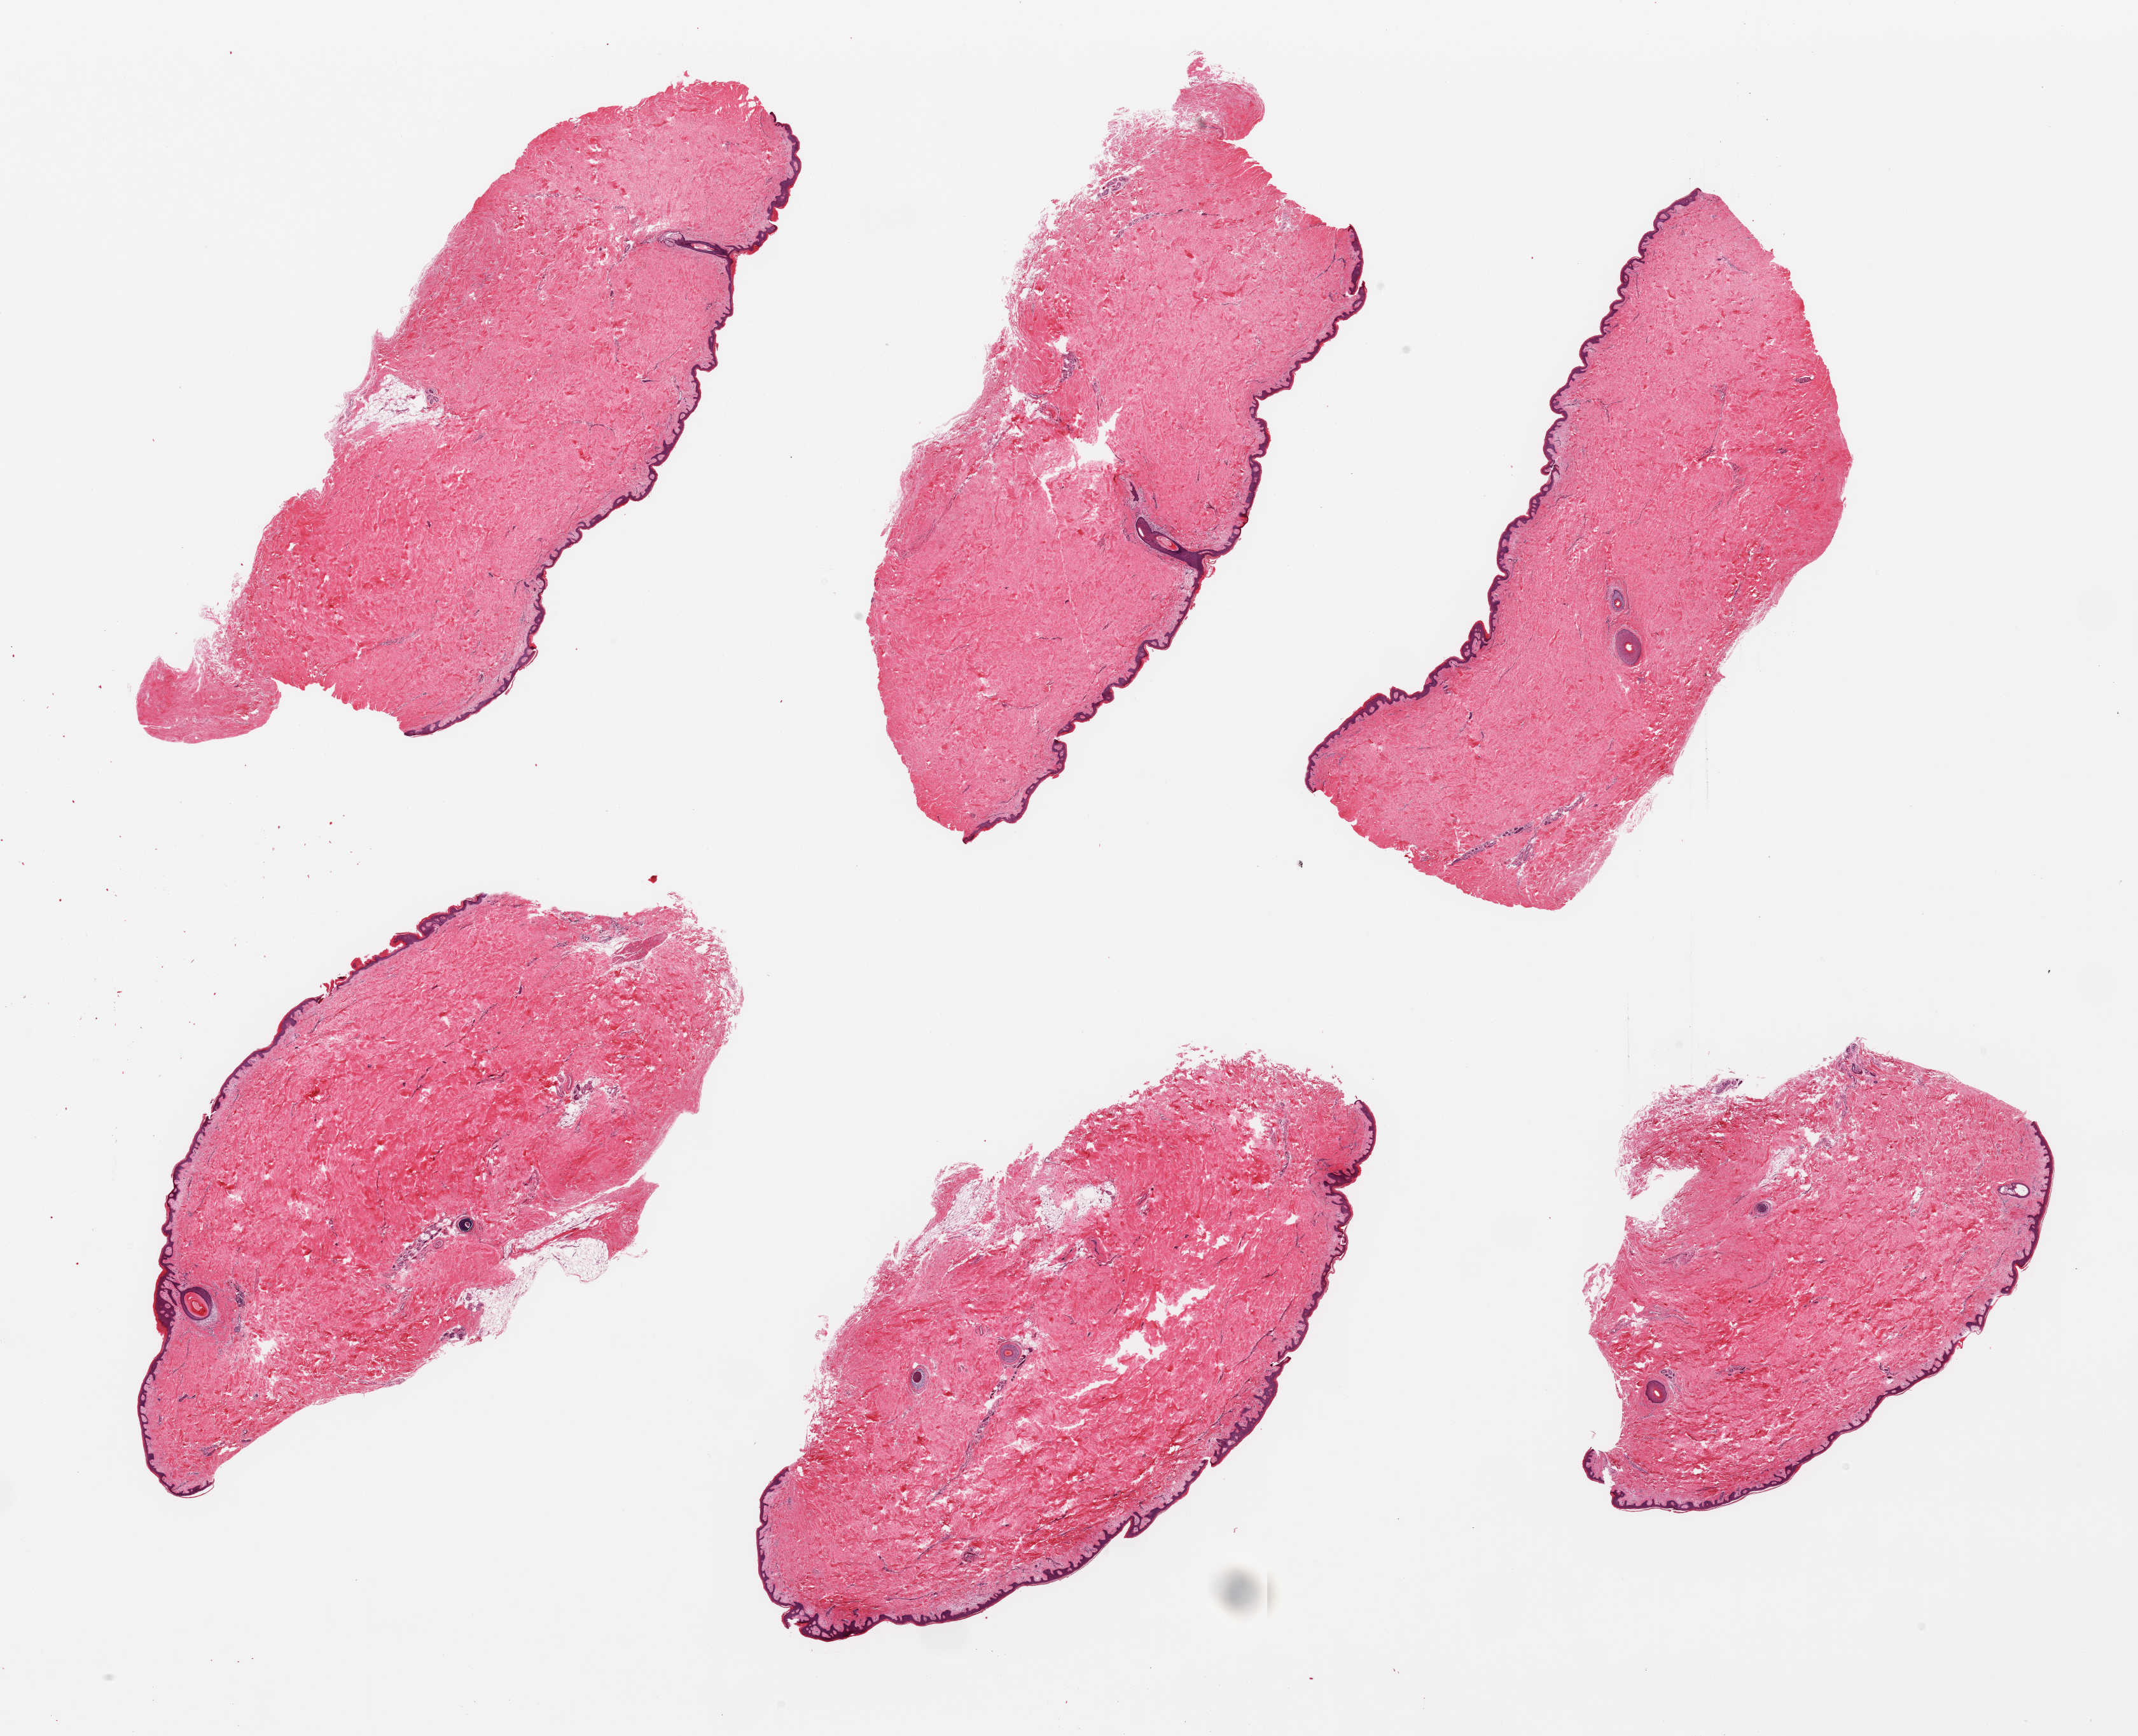
Whole-slide image, haematoxylin and eosin stain, brightfield, whole scanned area (about 26.6 x 21.6 mm, from a 20x scan) shown as a low-resolution overview. PAXgene-fixed, paraffin-embedded tissue. Target tissue: skin of suprapubic region. Tissue donor sample. Donor: male.
Reviewer comment on this tissue sample: 6 pieces squamous epithelium is ~30-40 microns.